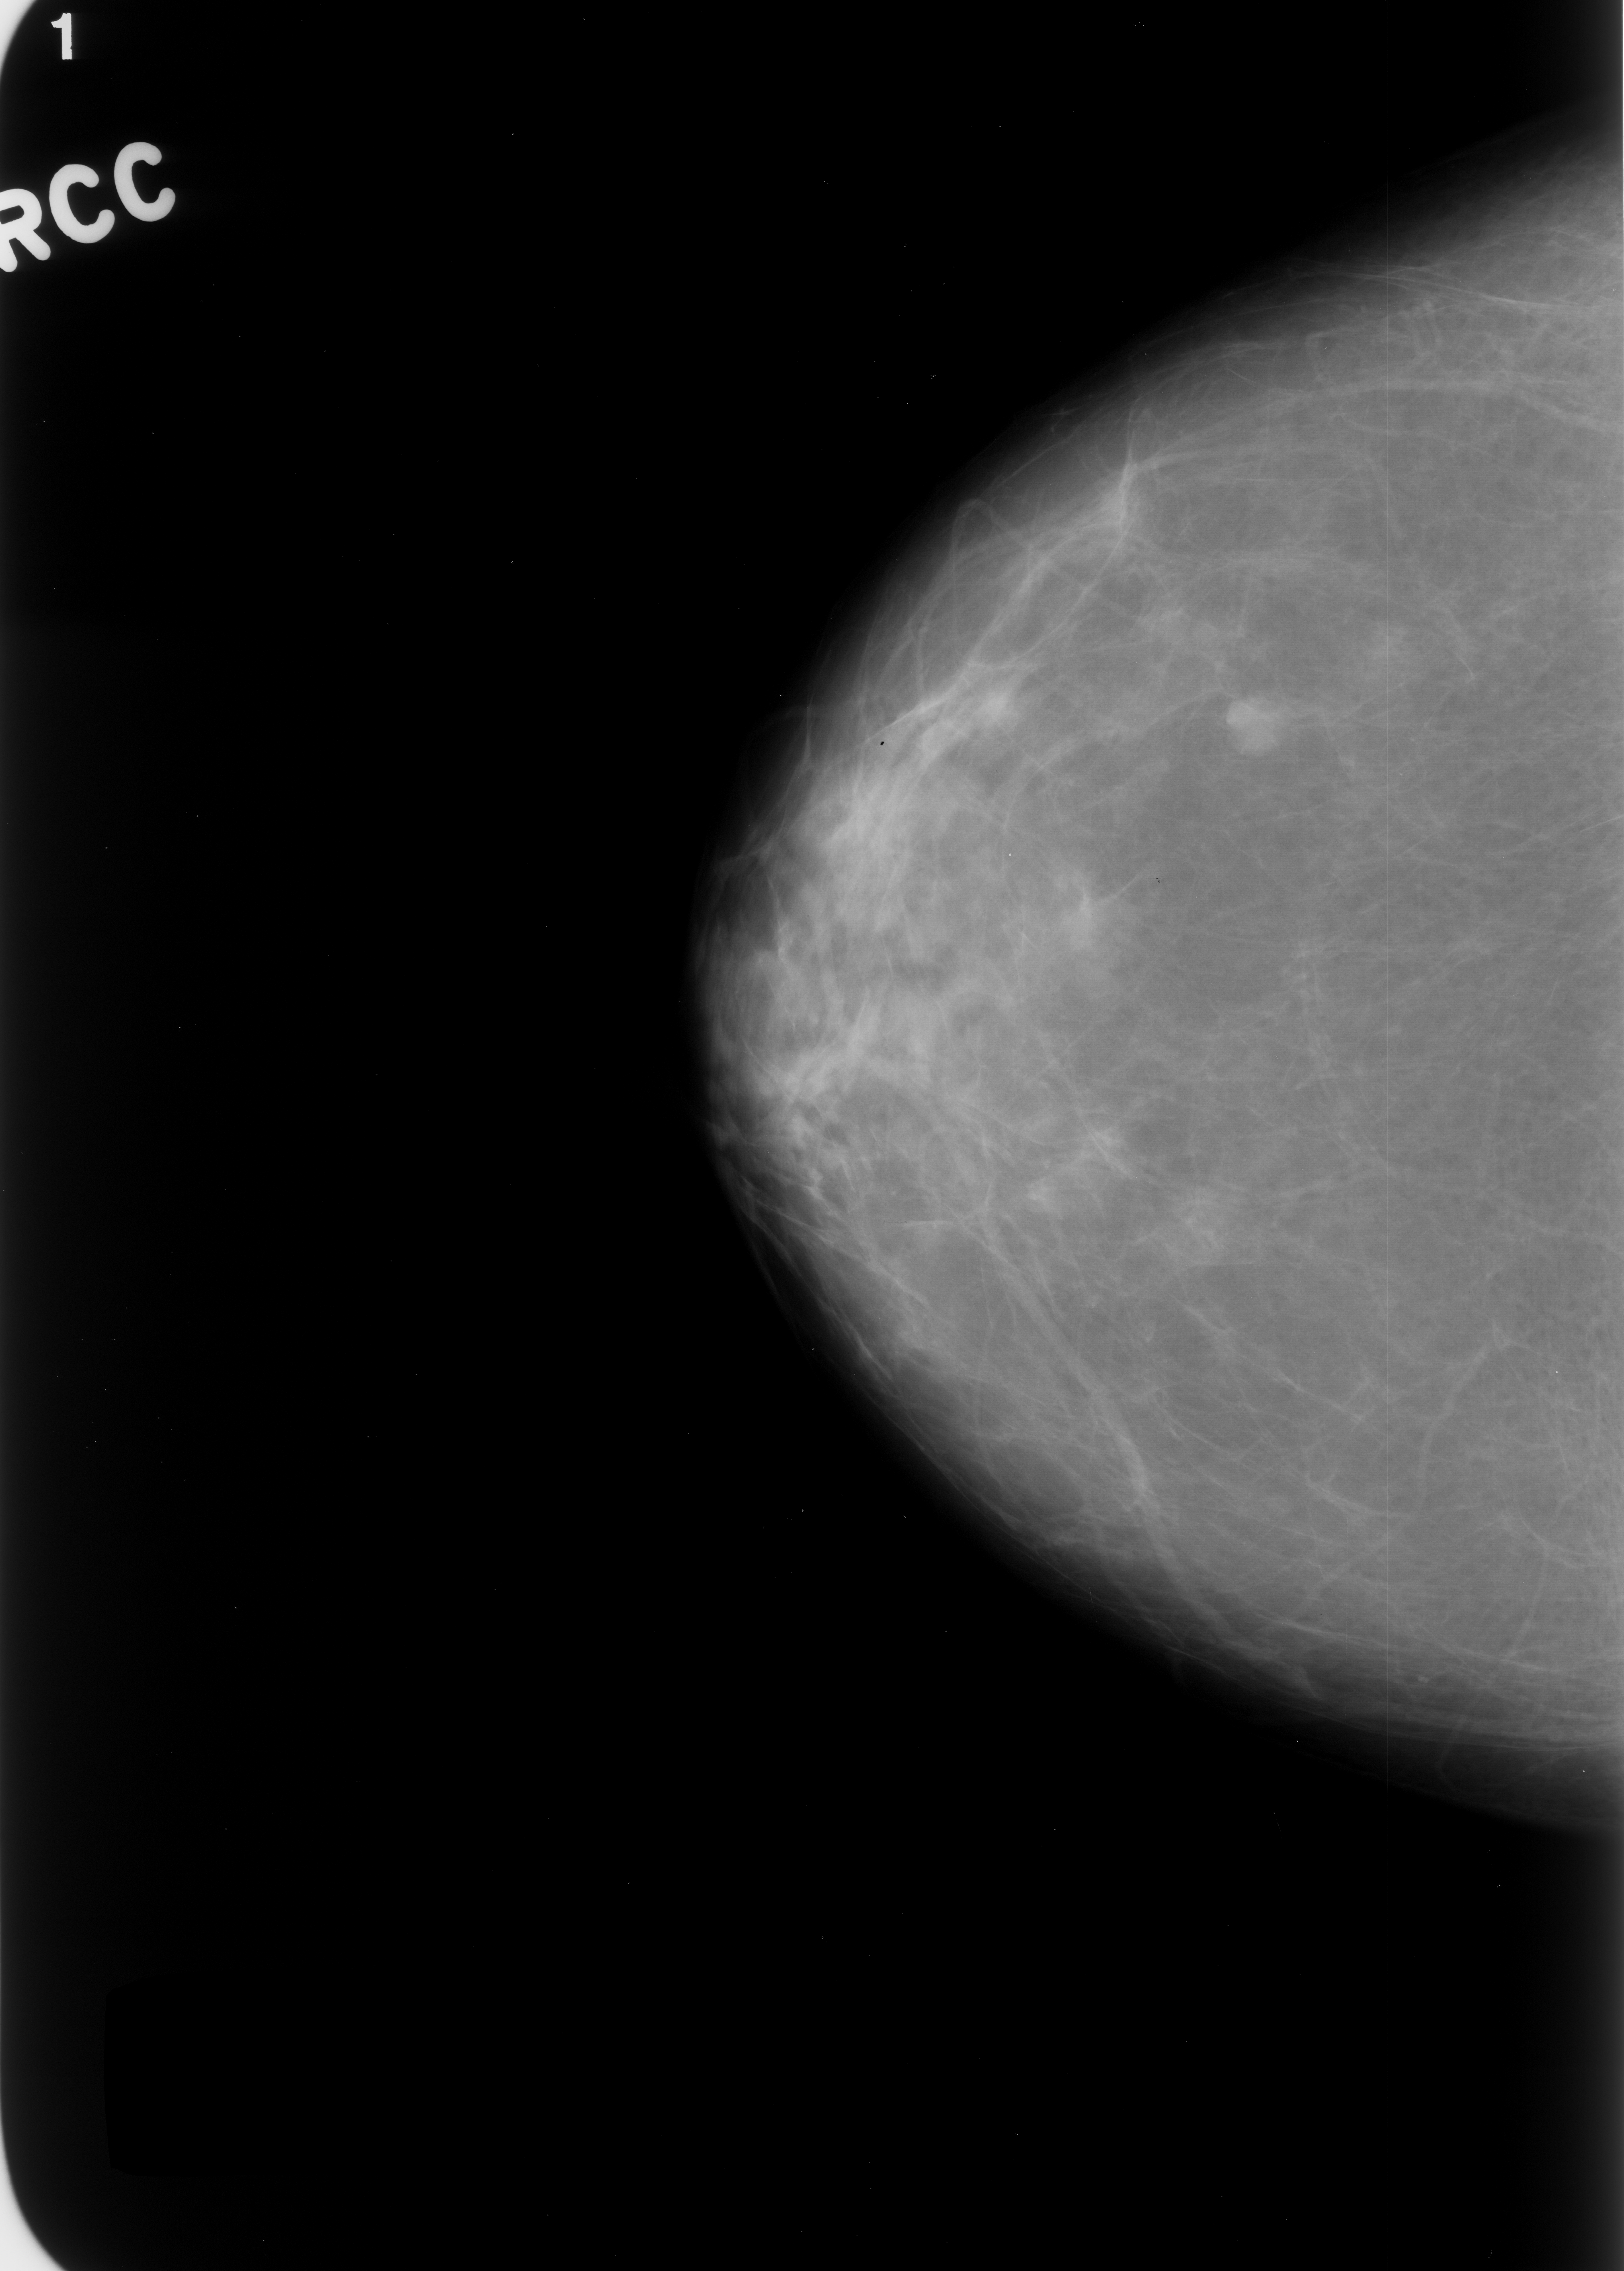
Scanned film-screen mammogram, right breast, craniocaudal (CC) view.
Abnormality record for this image: mass, shape lobulated, margins circumscribed; BI-RADS assessment category 2; subtlety rating 5 on a 1 (subtle) to 5 (obvious) scale; benign; no additional work-up was recommended (benign without callback).